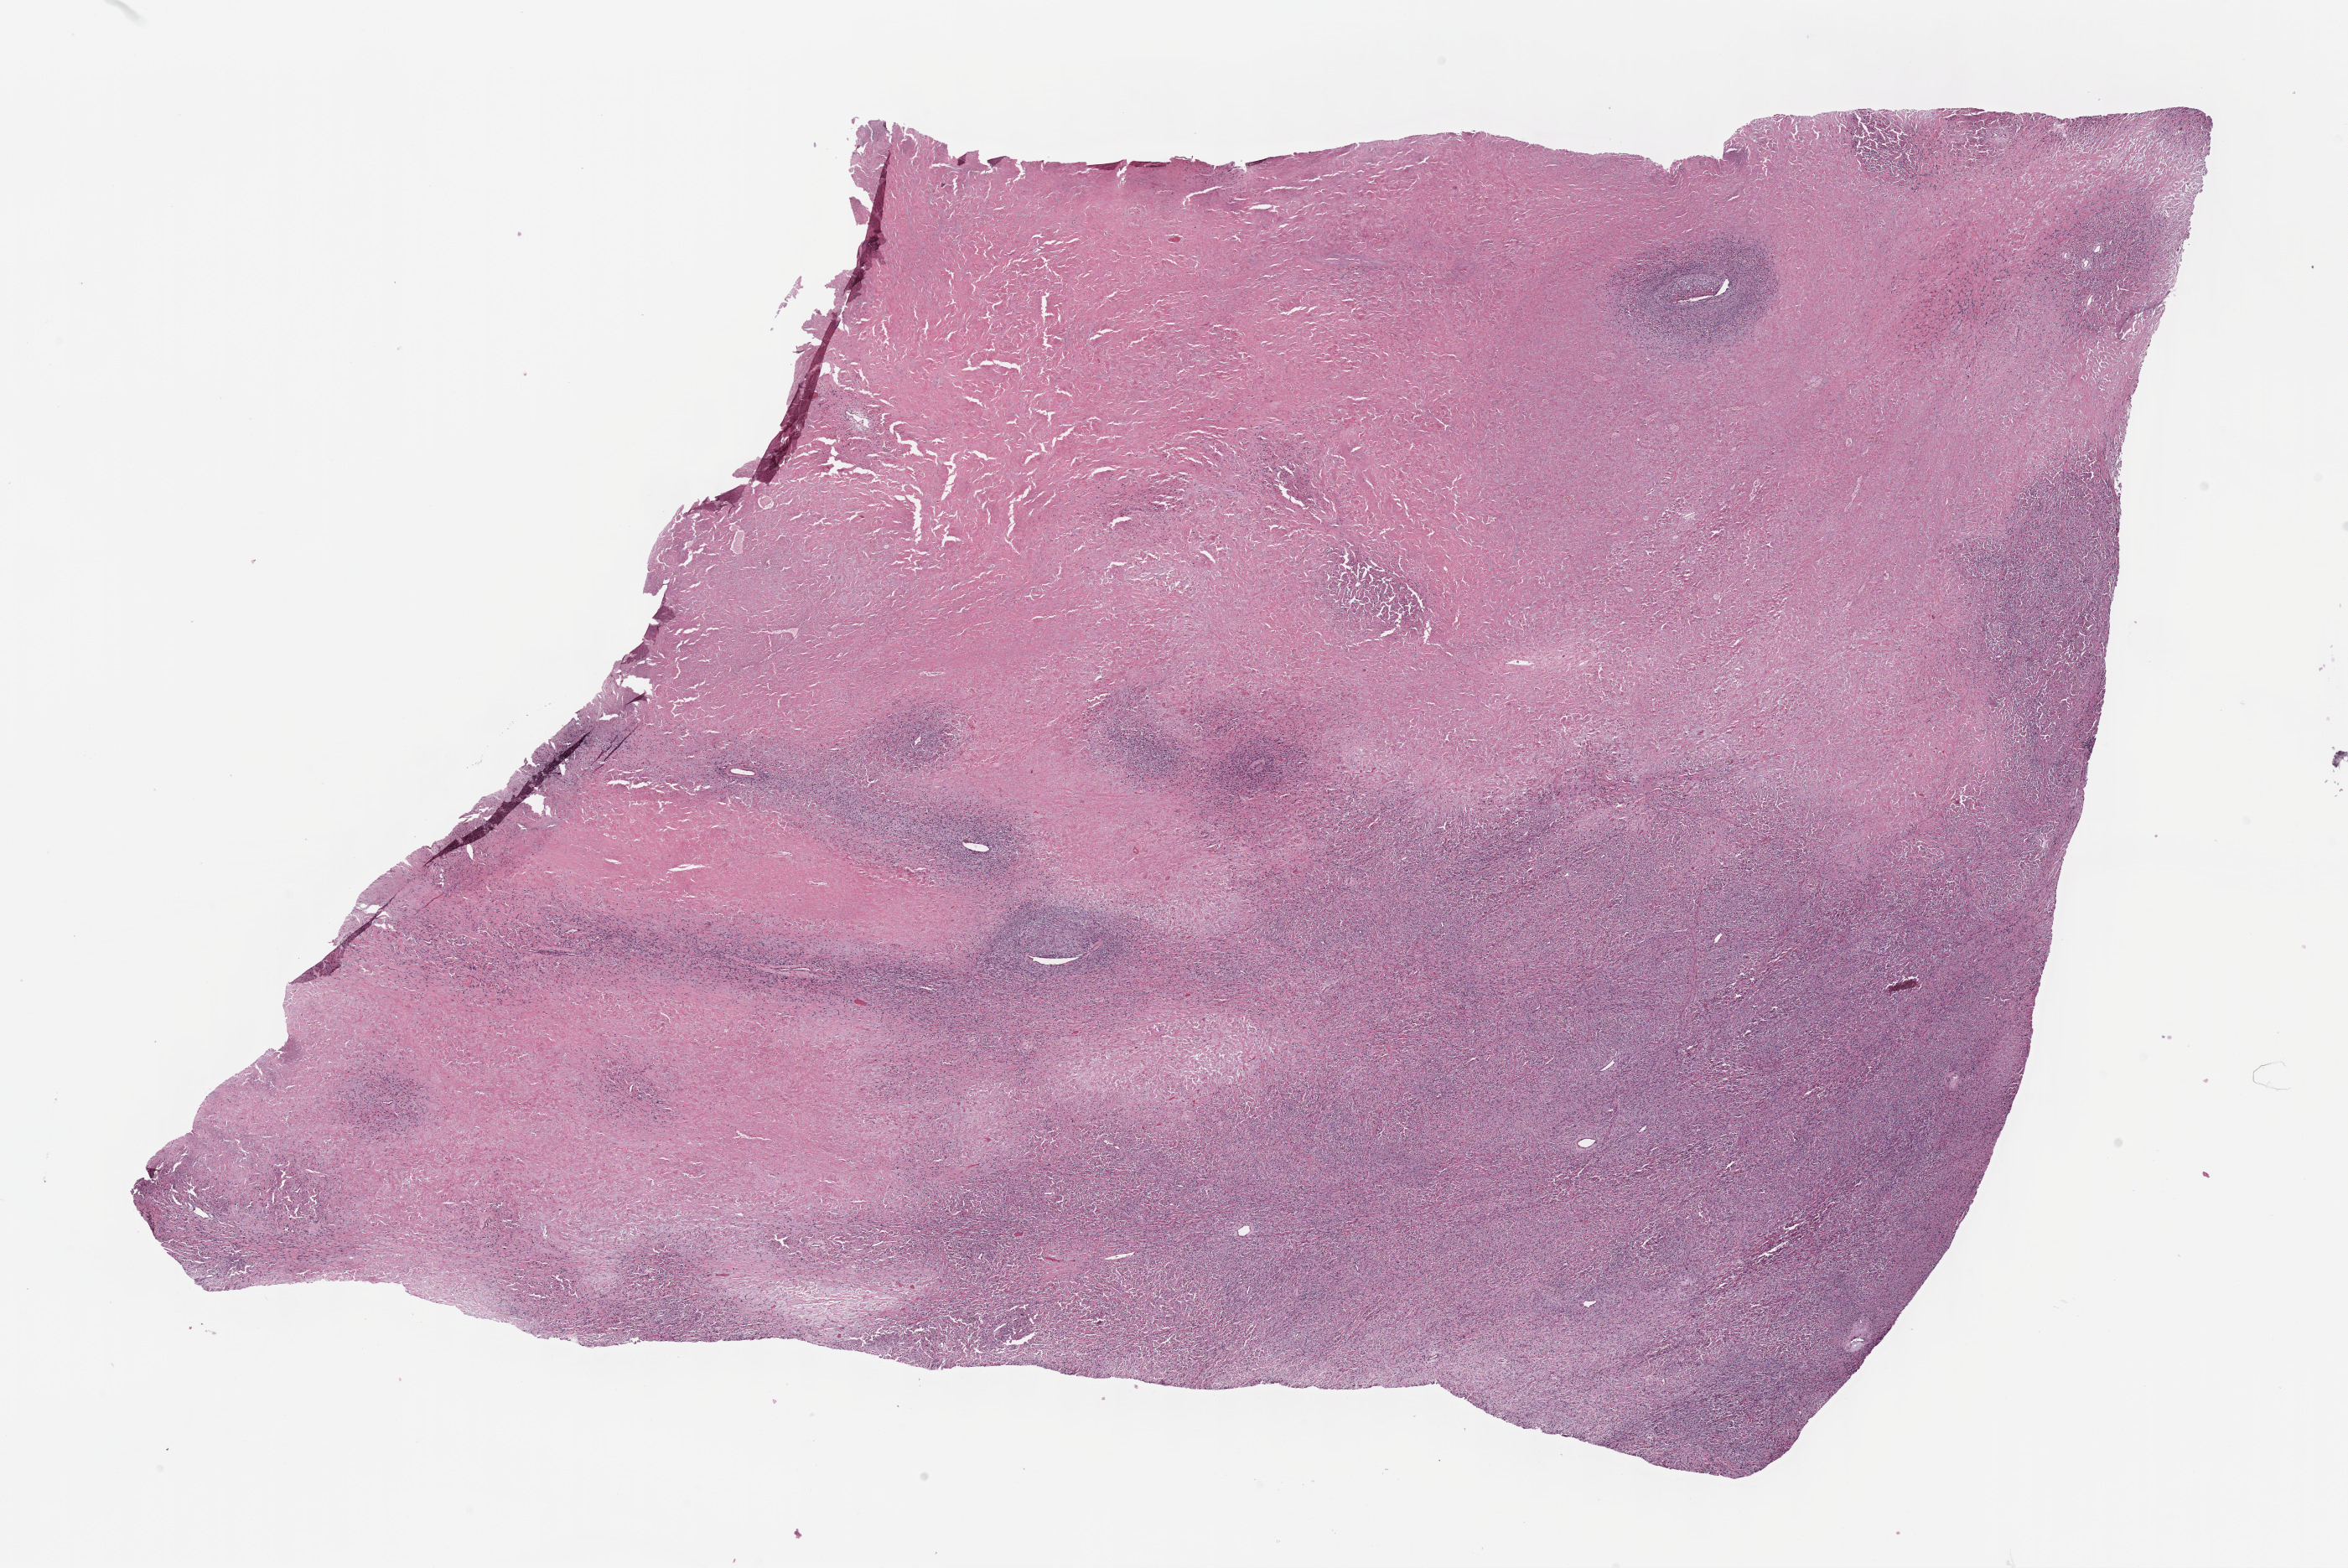
H&E whole-slide image, a low-resolution overview of the entire scanned area, about 22.7 x 15.1 mm (acquisition: 40x scan); formalin-fixed paraffin-embedded (FFPE) diagnostic section; connective, subcutaneous and other soft tissues, primary tumour sample. Female patient; age at initial diagnosis 20 years.
Pathologic diagnosis: Malignant peripheral nerve sheath tumor (connective, subcutaneous and other soft tissues of lower limb and hip).